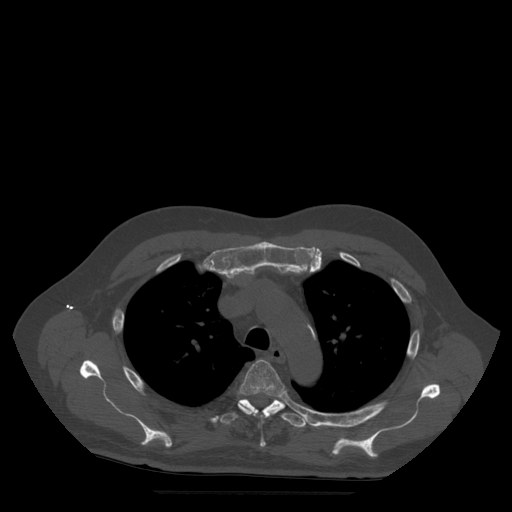
CT including the spine, one axial slice. Slice 384 of 522 in the series (ordered by position). Bone window (W 1800 / L 400 HU). 1.25 mm slice thickness. 512 × 512 image matrix, field of view 420 × 420 mm. Patient age 72 years. Case-level facts recorded for this patient, not image findings: primary cancer: prostate.
Annotated regions visible in this slice (semi-automatically segmented with operator editing):
- T4 vertebra: bounding box [x1, y1, x2, y2] px = [239, 360, 288, 448]
- T5 vertebra: [220, 395, 312, 428]